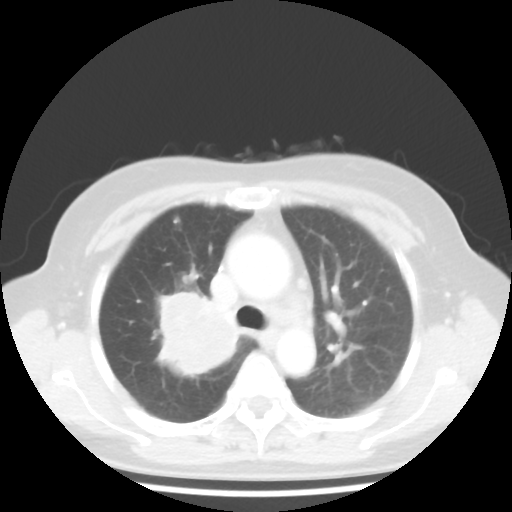
Chest CT, one axial slice; 100 kVp; lung window (W 1500 / L -600 HU); 5 mm slice thickness; 512 × 512 image matrix. Patient: female, 62 years. Case-level facts recorded for this patient, not image findings: clinical TNM (as recorded): T3 N0 M0; histopathological grade: G3.
Structures marked on this image (bounding box drawn by a radiologist):
- lung tumour (recorded histology: small cell carcinoma): bounding box (x1, y1, x2, y2) in pixels: (145, 282, 243, 388)